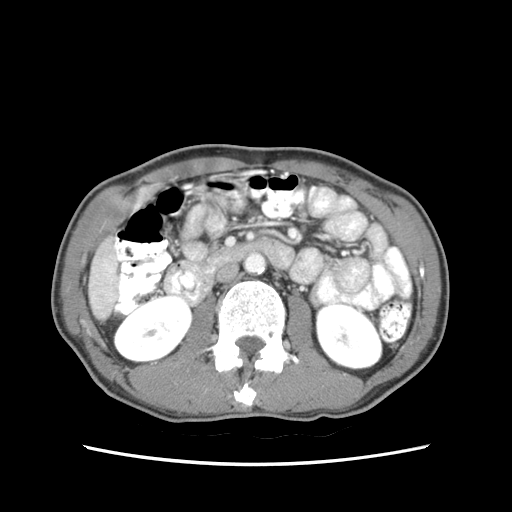
Contrast-enhanced abdominal CT (liver protocol), one axial slice; position 13 of 79 along the scan axis; reconstruction kernel STANDARD; soft-tissue window (W 400 / L 40 HU); 2.5 mm slice thickness; 512 × 512 image matrix. Case-level facts recorded for this patient, not image findings: diagnosis: hepatocellular carcinoma (patient treated with transarterial chemoembolisation; whether this scan precedes or follows treatment is not stated here); TNM stage (as recorded): Stage-IIIB; Child-Pugh class: A; tumour differentiation: moderately differentiated; tumour nodularity: multinodular.
Outlined on this slice (semi-automatically segmented with operator editing):
- liver parenchyma outside the tumour (the mass and vessels are separate outlines, so this box may not span the whole liver): bounding box <90,228,118,318> (left, top, right, bottom; pixels)
- liver vessels: <110,268,113,273>